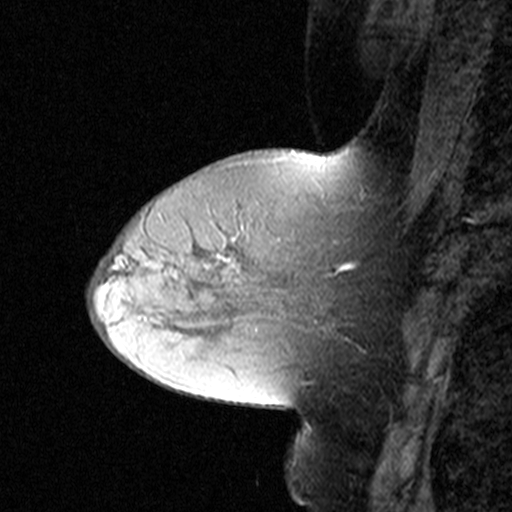
Breast MRI (dynamic contrast-enhanced), one sagittal slice. Position 15 of 44 along the scan axis. Dynamic contrast-enhanced study with each time point stored as its own series, time point 2 of 3 at this slice position (early post-contrast, ordered by acquisition time). 1.5 T. TE 4.5 ms, TR 11 ms. 3 mm slice thickness. 512 × 512 image matrix, field of view 200 × 200 mm. Female patient, age 50 years. Case-level facts recorded for this patient, not image findings: setting: breast cancer imaged before/during neoadjuvant chemotherapy; receptor status: HR-positive, HER2-negative.
Structures marked on this image (semi-automatic segmentation, software-assisted and operator-edited):
- analysis volume of interest (the breast-tissue region the enhancement analysis was run in; not a lesion): bounding box (x1, y1, x2, y2) in pixels: (180, 198, 314, 311)
- tumour enhancement mask (voxels above the 90 % enhancement threshold inside the analysis volume of interest): (219, 256, 238, 269)